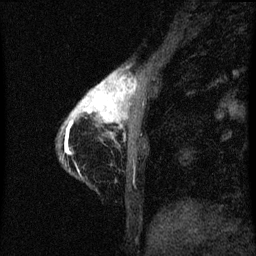
Breast MRI (dynamic contrast-enhanced), one sagittal slice; position 9 of 60 along the scan axis; dynamic contrast-enhanced series, image 2 of 3 at this slice position (ordered by acquisition); 1.5 T; TE 4.2 ms, TR 8 ms; 2 mm slice thickness; 256 × 256 image matrix, field of view 180 × 180 mm. Patient: female, 38 years.
Annotated regions visible in this slice (semi-automatically segmented with operator editing):
- analysis volume of interest (the breast-tissue region the enhancement analysis was run in; not a lesion): bounding box [x1, y1, x2, y2] px = [61, 72, 141, 147]
- tumour enhancement mask (voxels above the 70 % enhancement threshold inside the analysis volume of interest): [65, 74, 133, 145]